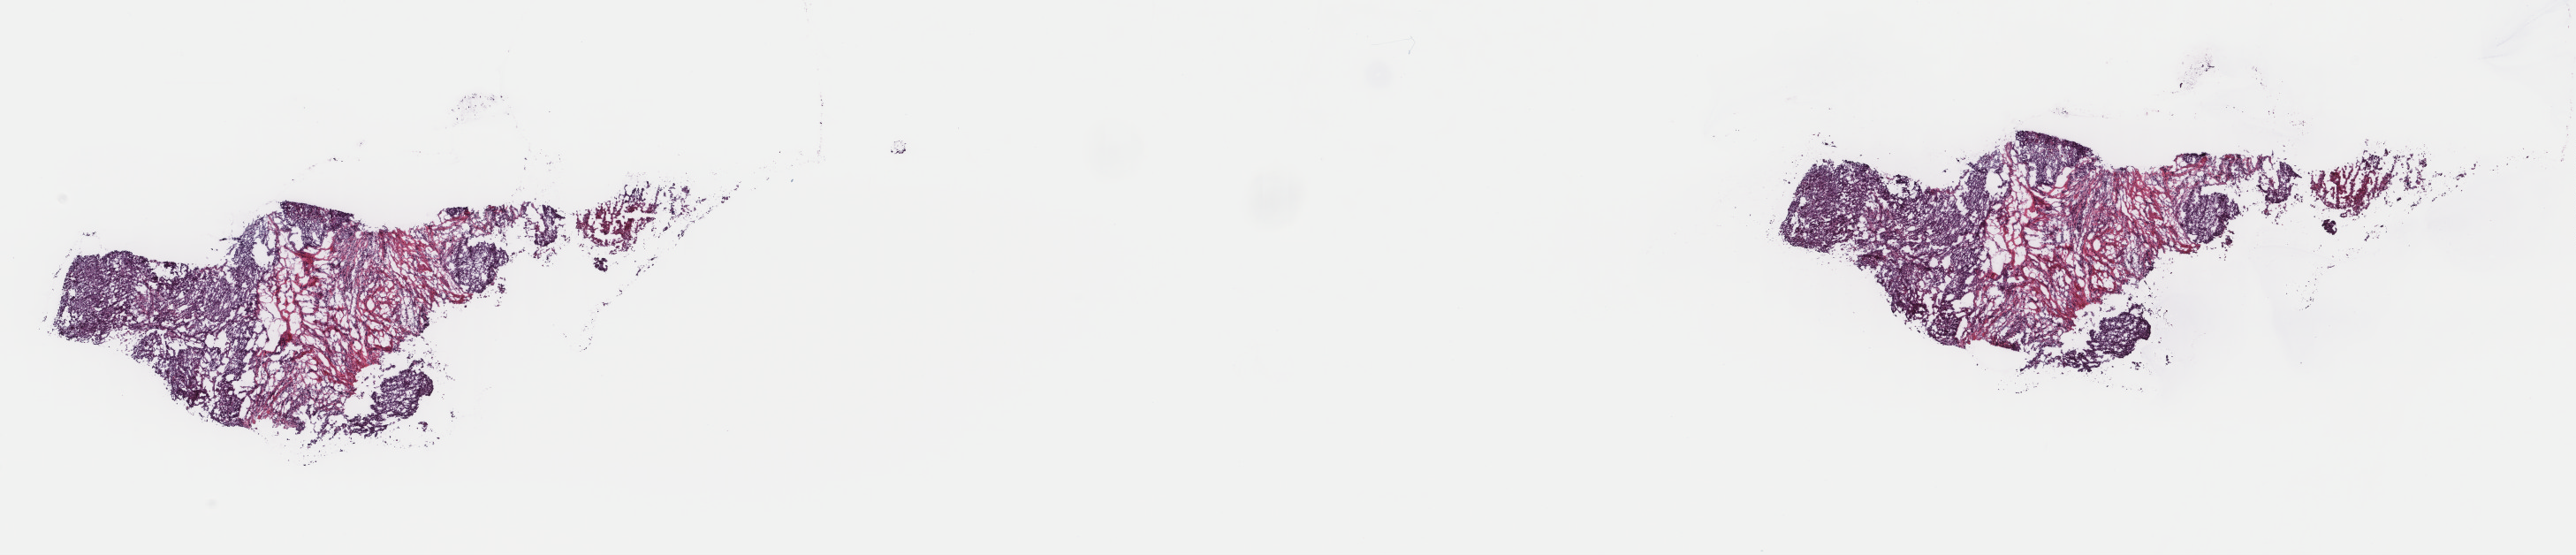
Digitized H&E tissue section (whole slide) — a low-resolution overview of the entire scanned area, about 23.1 x 5.0 mm (slide scanned at 40x), frozen section from the top of the tissue portion, primary tumour sample from the cervix. Female patient; age at initial diagnosis 60 years. Histologic grade: G2 (moderately differentiated). Pathologist review of this section (percent, as recorded): tumour cells 80%, tumour nuclei 90%, normal cells 20%, stromal cells 0%, necrosis 0%. Inflammatory infiltration, as recorded: lymphocyte infiltration 2%, monocyte infiltration 0%, neutrophil infiltration 0%.
- lymph nodes positive (case pathology): 0 of 15 examined
- FIGO stage: IB1
- histologic diagnosis: Squamous cell carcinoma, NOS (cervix uteri)